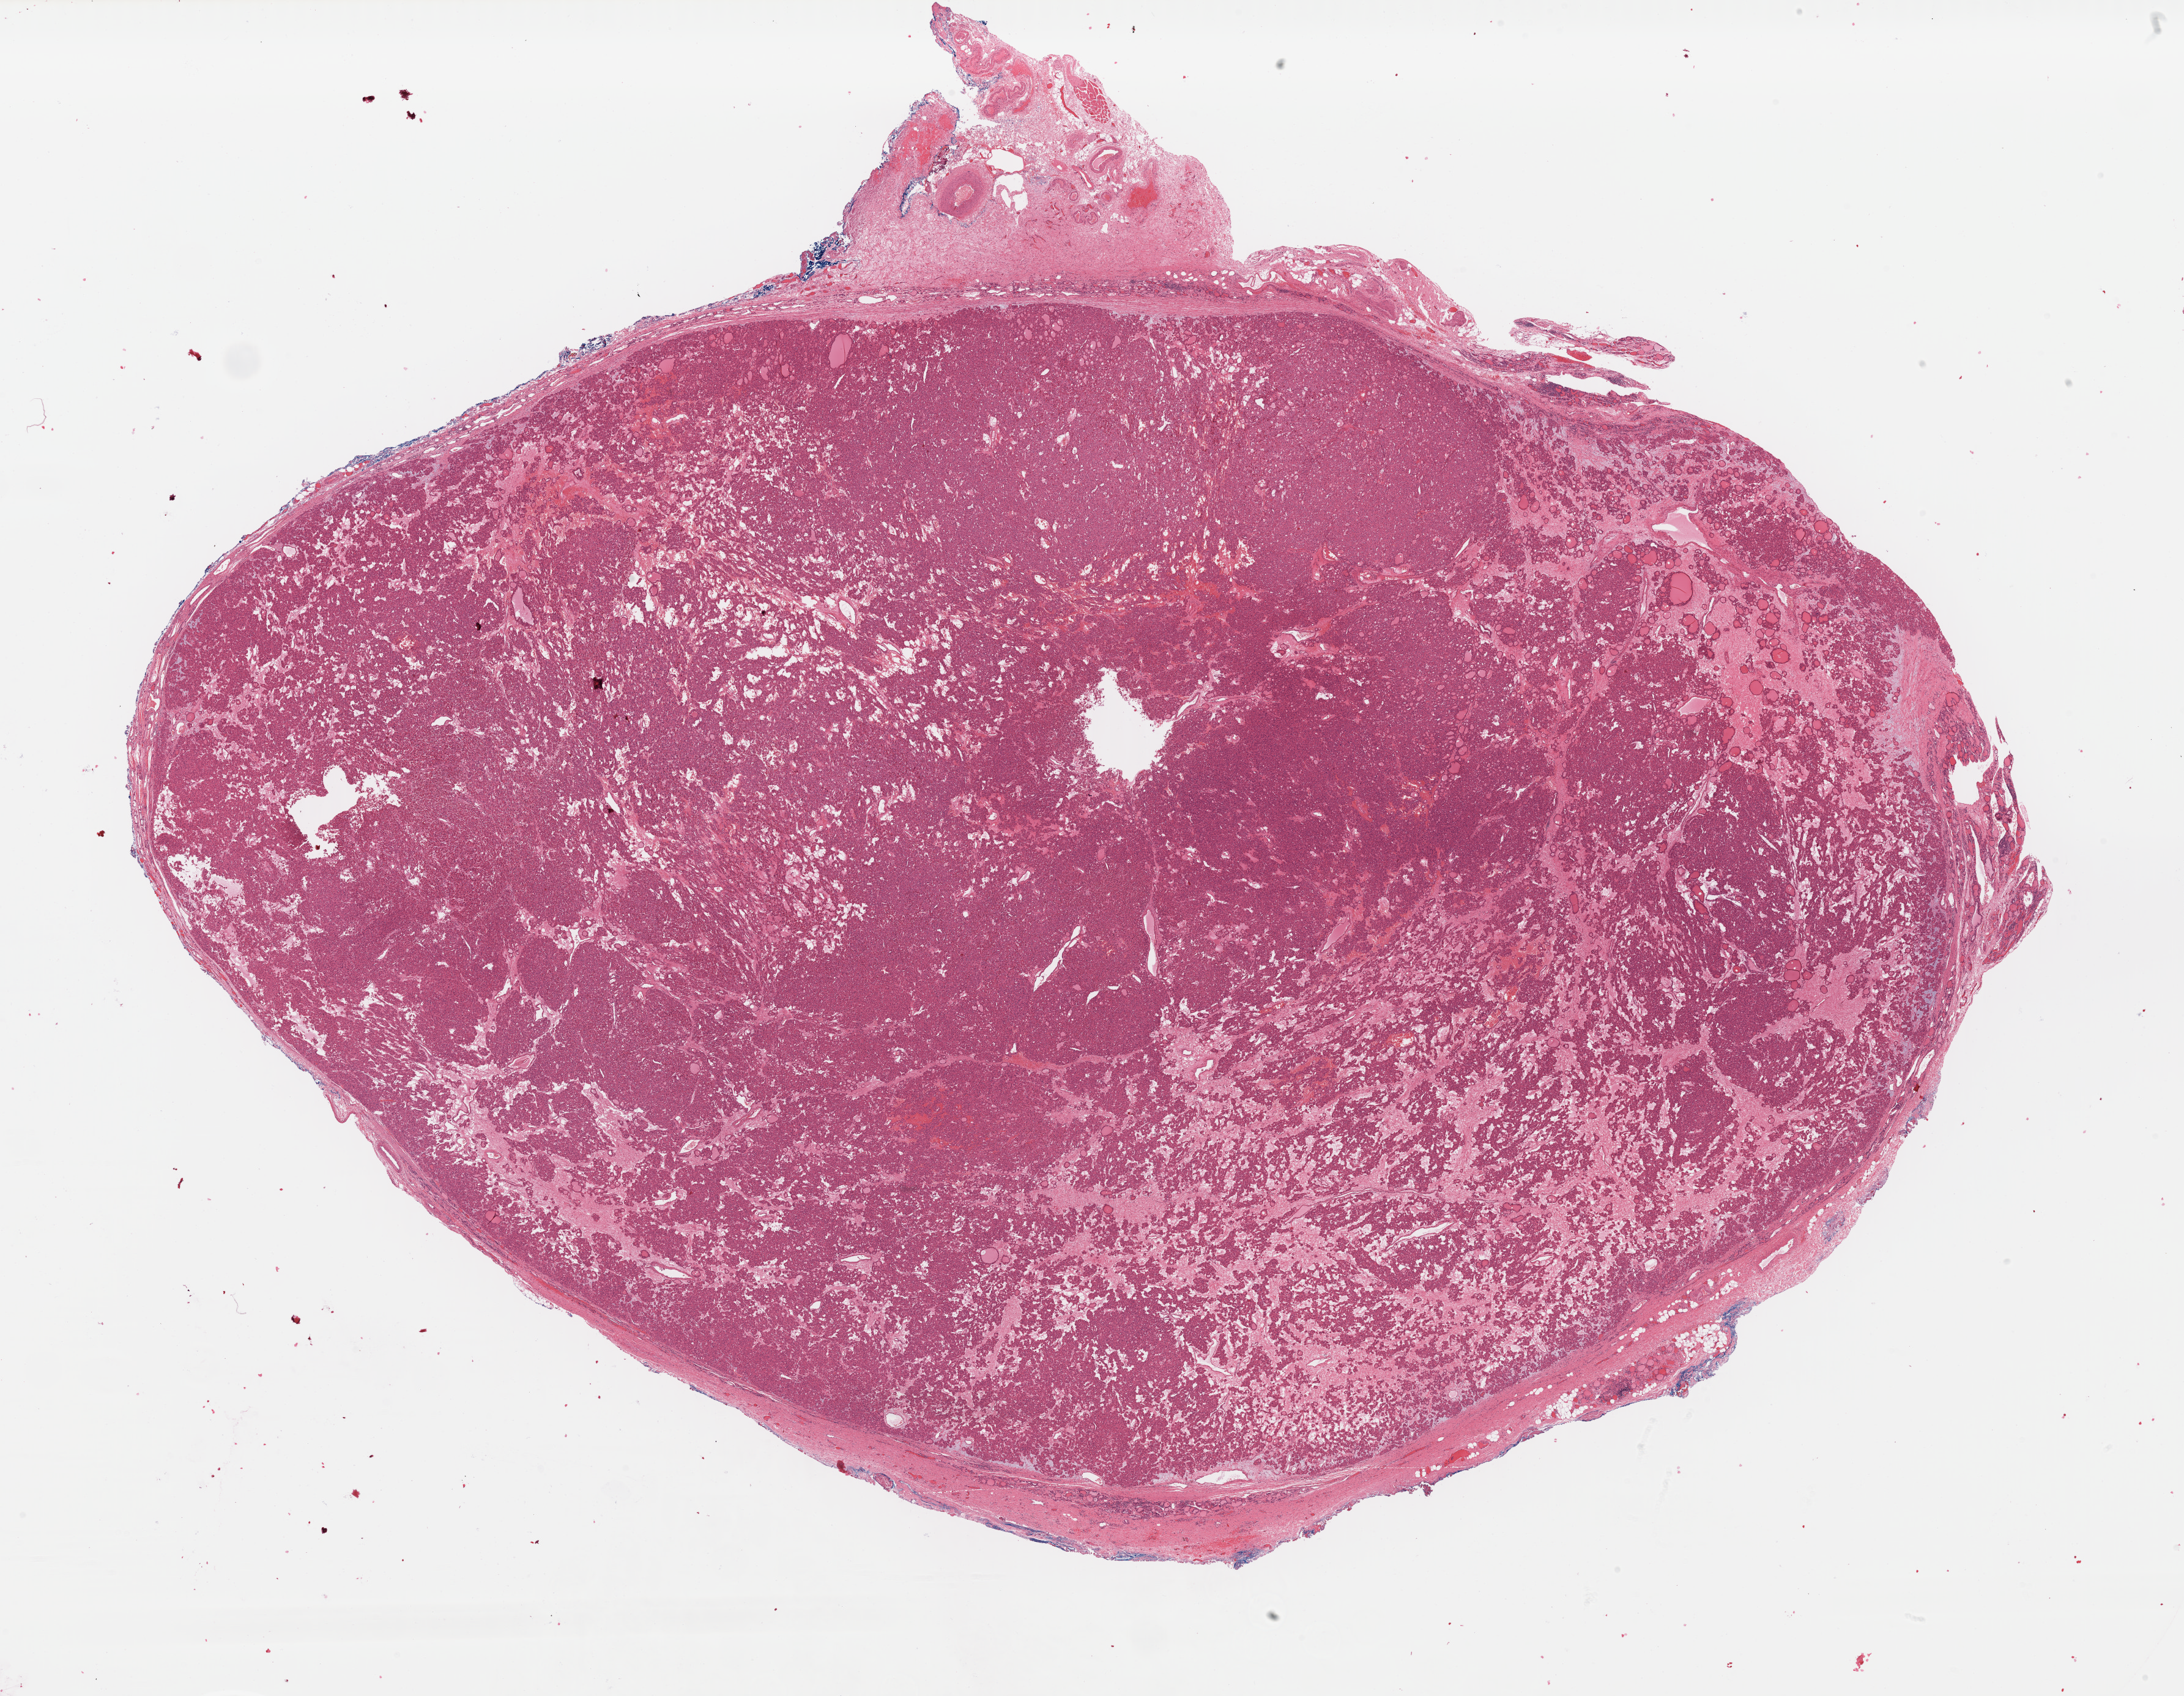
H&E-stained whole-slide image — low-resolution overview of the scanned area, about 28.2 x 21.9 mm (acquisition: 40x scan), formalin-fixed paraffin-embedded (FFPE) diagnostic section, thyroid, primary tumour sample. Patient: female, age at initial diagnosis 73 years.
* histologic diagnosis: Papillary carcinoma, follicular variant
* AJCC pathologic stage: II (7th edition)